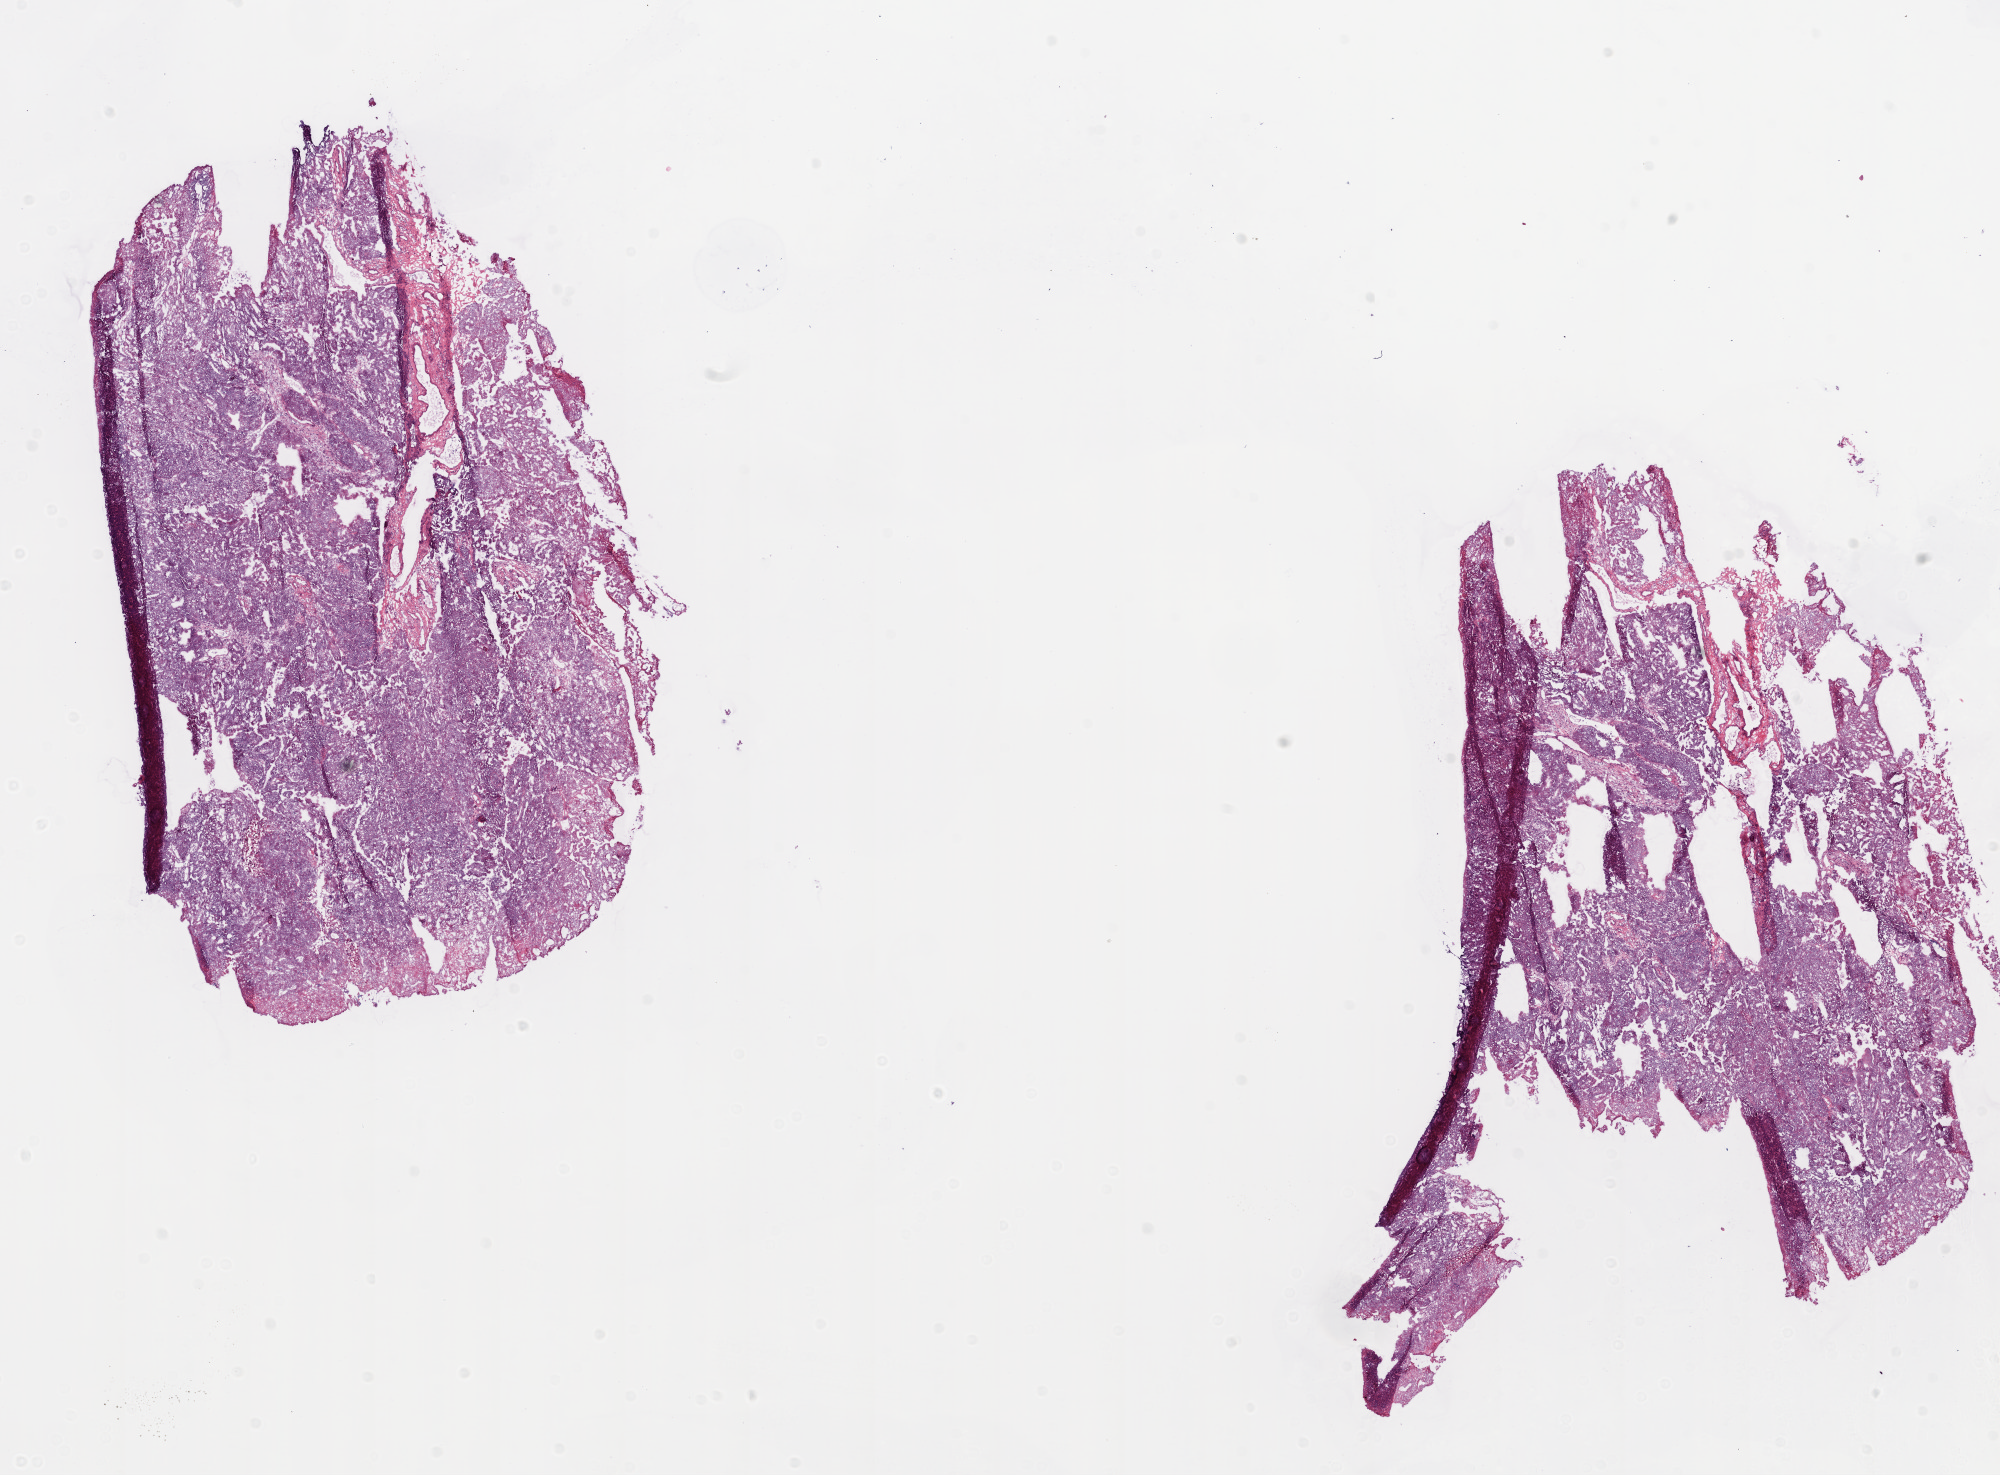
Digitized Hematoxylin and eosin (H&E) stained tissue section (whole slide) — shown as a low-resolution overview of the whole scanned area (about 16.0 x 11.8 mm, slide scanned at 20x). Frozen section from the top of the tissue portion. Primary tumour sample from the ovary. Patient: female, age at initial diagnosis 85 years. Histologic grade: G3 (poorly differentiated). Slide review estimates, as recorded: tumour cells 90%, tumour nuclei 95%, normal cells 0%, stromal cells 5%, necrosis 5%.
- diagnosis: Serous cystadenocarcinoma, NOS
- FIGO stage: IIIC